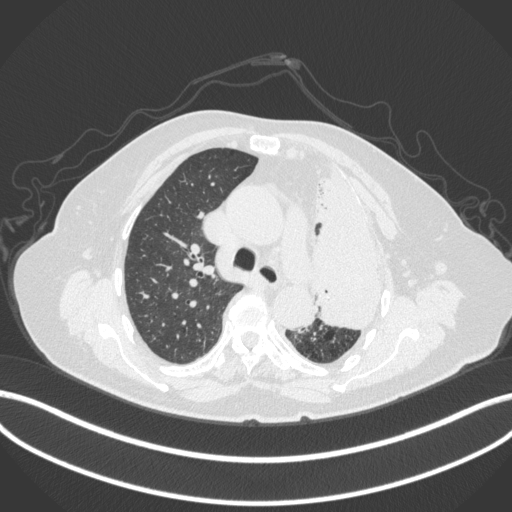
Chest CT, one axial slice; slice 272 of 399 in the series (ordered by position); reconstruction kernel B31f; lung window (W 1500 / L -600 HU); 512 × 512 image matrix, field of view 400 × 400 mm. Female patient, age 75 years. Case-level facts recorded for this patient, not image findings: clinical TNM (as recorded): T3 N3 M1.
Annotated regions visible in this slice (bounding box drawn by a radiologist):
- lung tumour (recorded histology: adenocarcinoma): bounding box <311,158,391,335> (left, top, right, bottom; pixels)